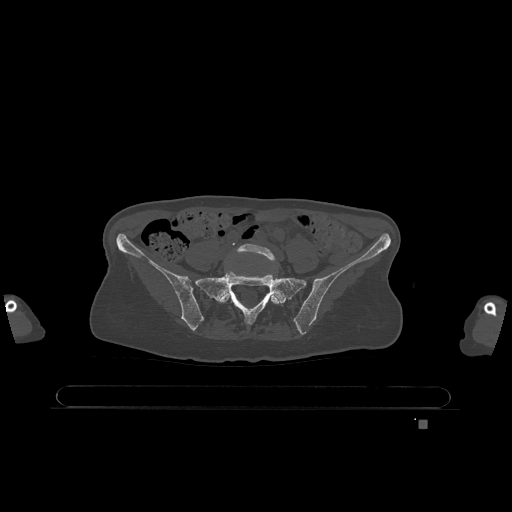
CT including the spine, one axial slice; slice 207 of 1317 in the series (ordered by position); bone window (W 1800 / L 400 HU); 0.5 mm slice thickness; 512 × 512 image matrix, field of view 500 × 500 mm. Patient: female, 74 years. Case-level facts recorded for this patient, not image findings: primary cancer: lung.
Annotated regions visible in this slice (semi-automatic segmentation, software-assisted and operator-edited):
- L5 vertebra: bounding box <219,244,283,306> (left, top, right, bottom; pixels)